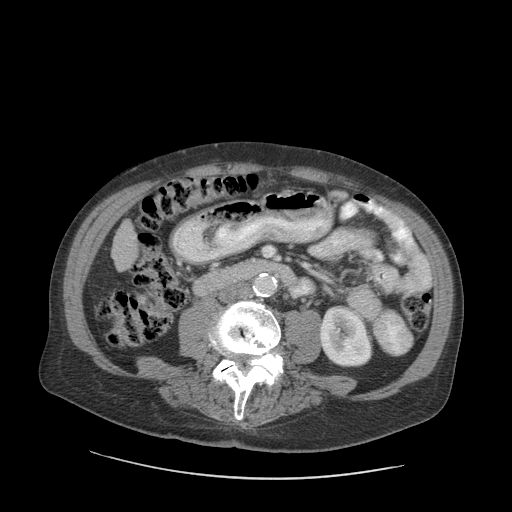
Contrast-enhanced abdominal CT (liver protocol), one axial slice; position 19 of 89 along the scan axis; reconstruction kernel STANDARD; soft-tissue window (W 400 / L 40 HU); 2.5 mm slice thickness; 512 × 512 image matrix, field of view 420 × 420 mm. From the clinical record (not read from this slice): diagnosis: hepatocellular carcinoma (patient treated with transarterial chemoembolisation; whether this scan precedes or follows treatment is not stated here); TNM stage (as recorded): Stage-I; Child-Pugh class: A; tumour differentiation: moderately differentiated; tumour size: 4.6 cm.
Outlined on this slice (semi-automatically segmented with operator editing):
- liver parenchyma outside the tumour (the mass and vessels are separate outlines, so this box may not span the whole liver): bounding box (x1, y1, x2, y2) in pixels: (112, 220, 138, 271)